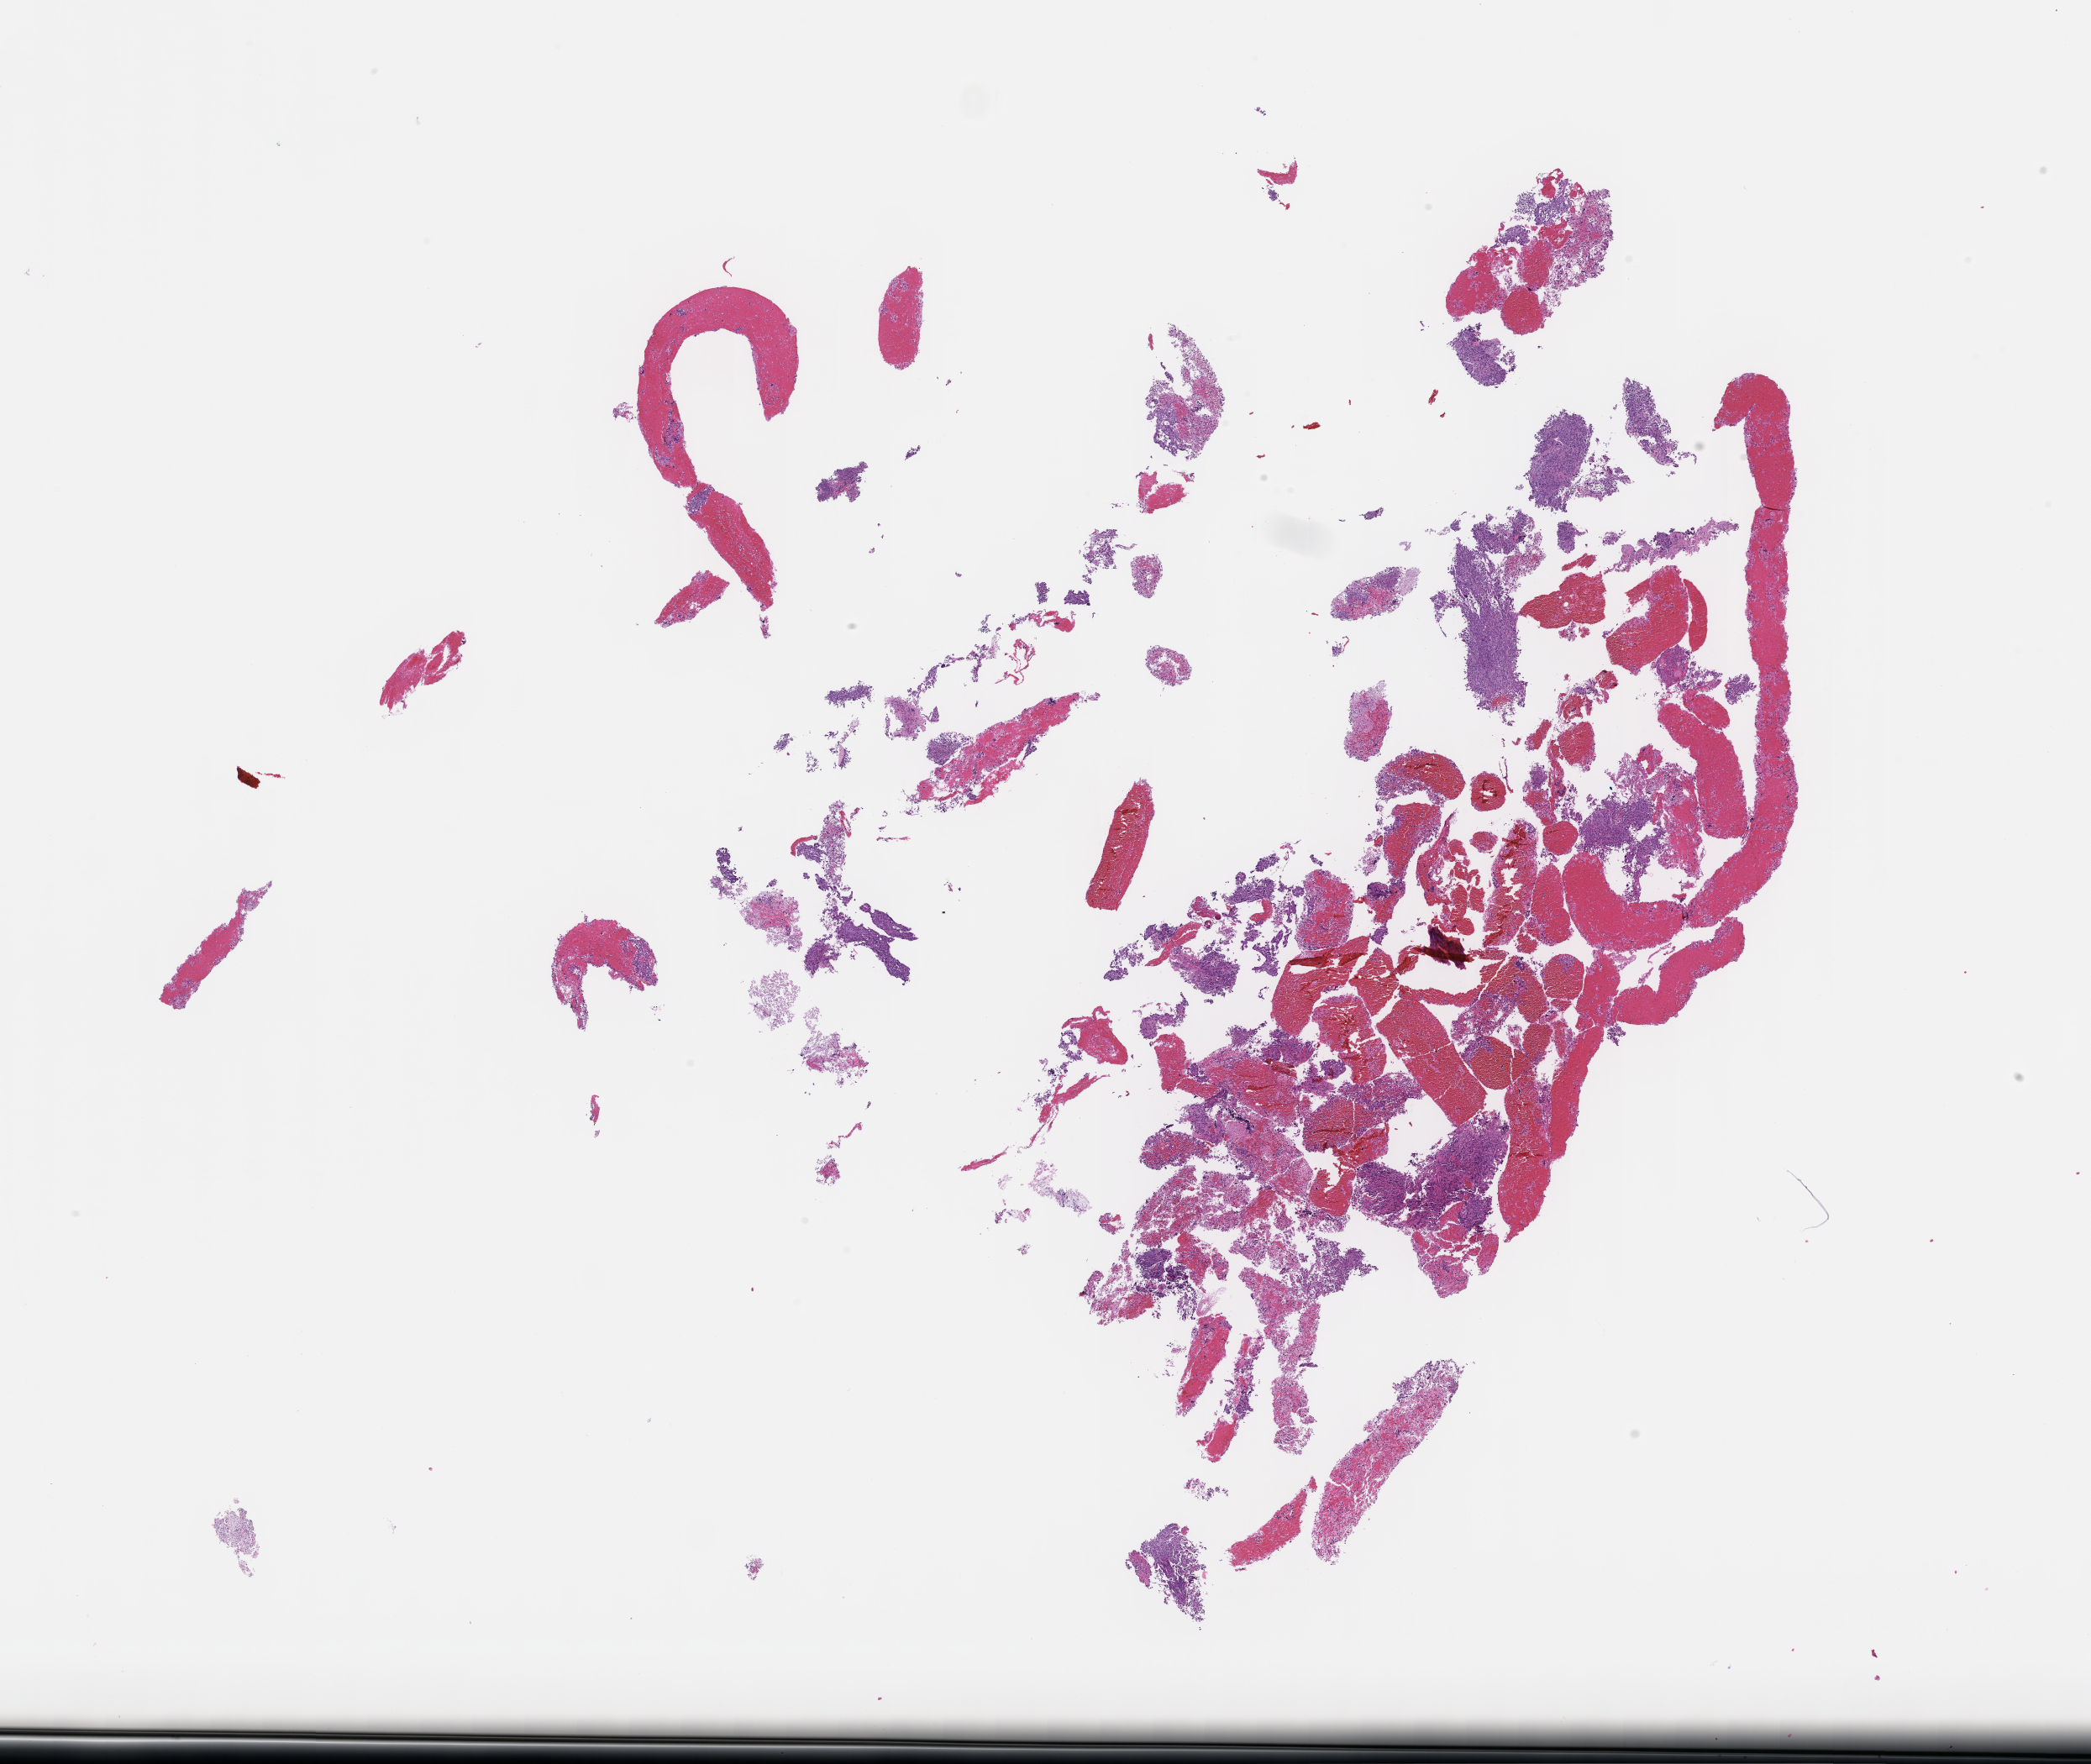
H&E whole-slide image, a low-resolution overview of the entire scanned area, about 20.1 x 17.0 mm, formalin-fixed paraffin-embedded section, specimen time point: archival tissue. Patient: male.
This section: metastatic tumor tissue. Patient diagnosis (primary): Non-Small Cell Lung Carcinoma.